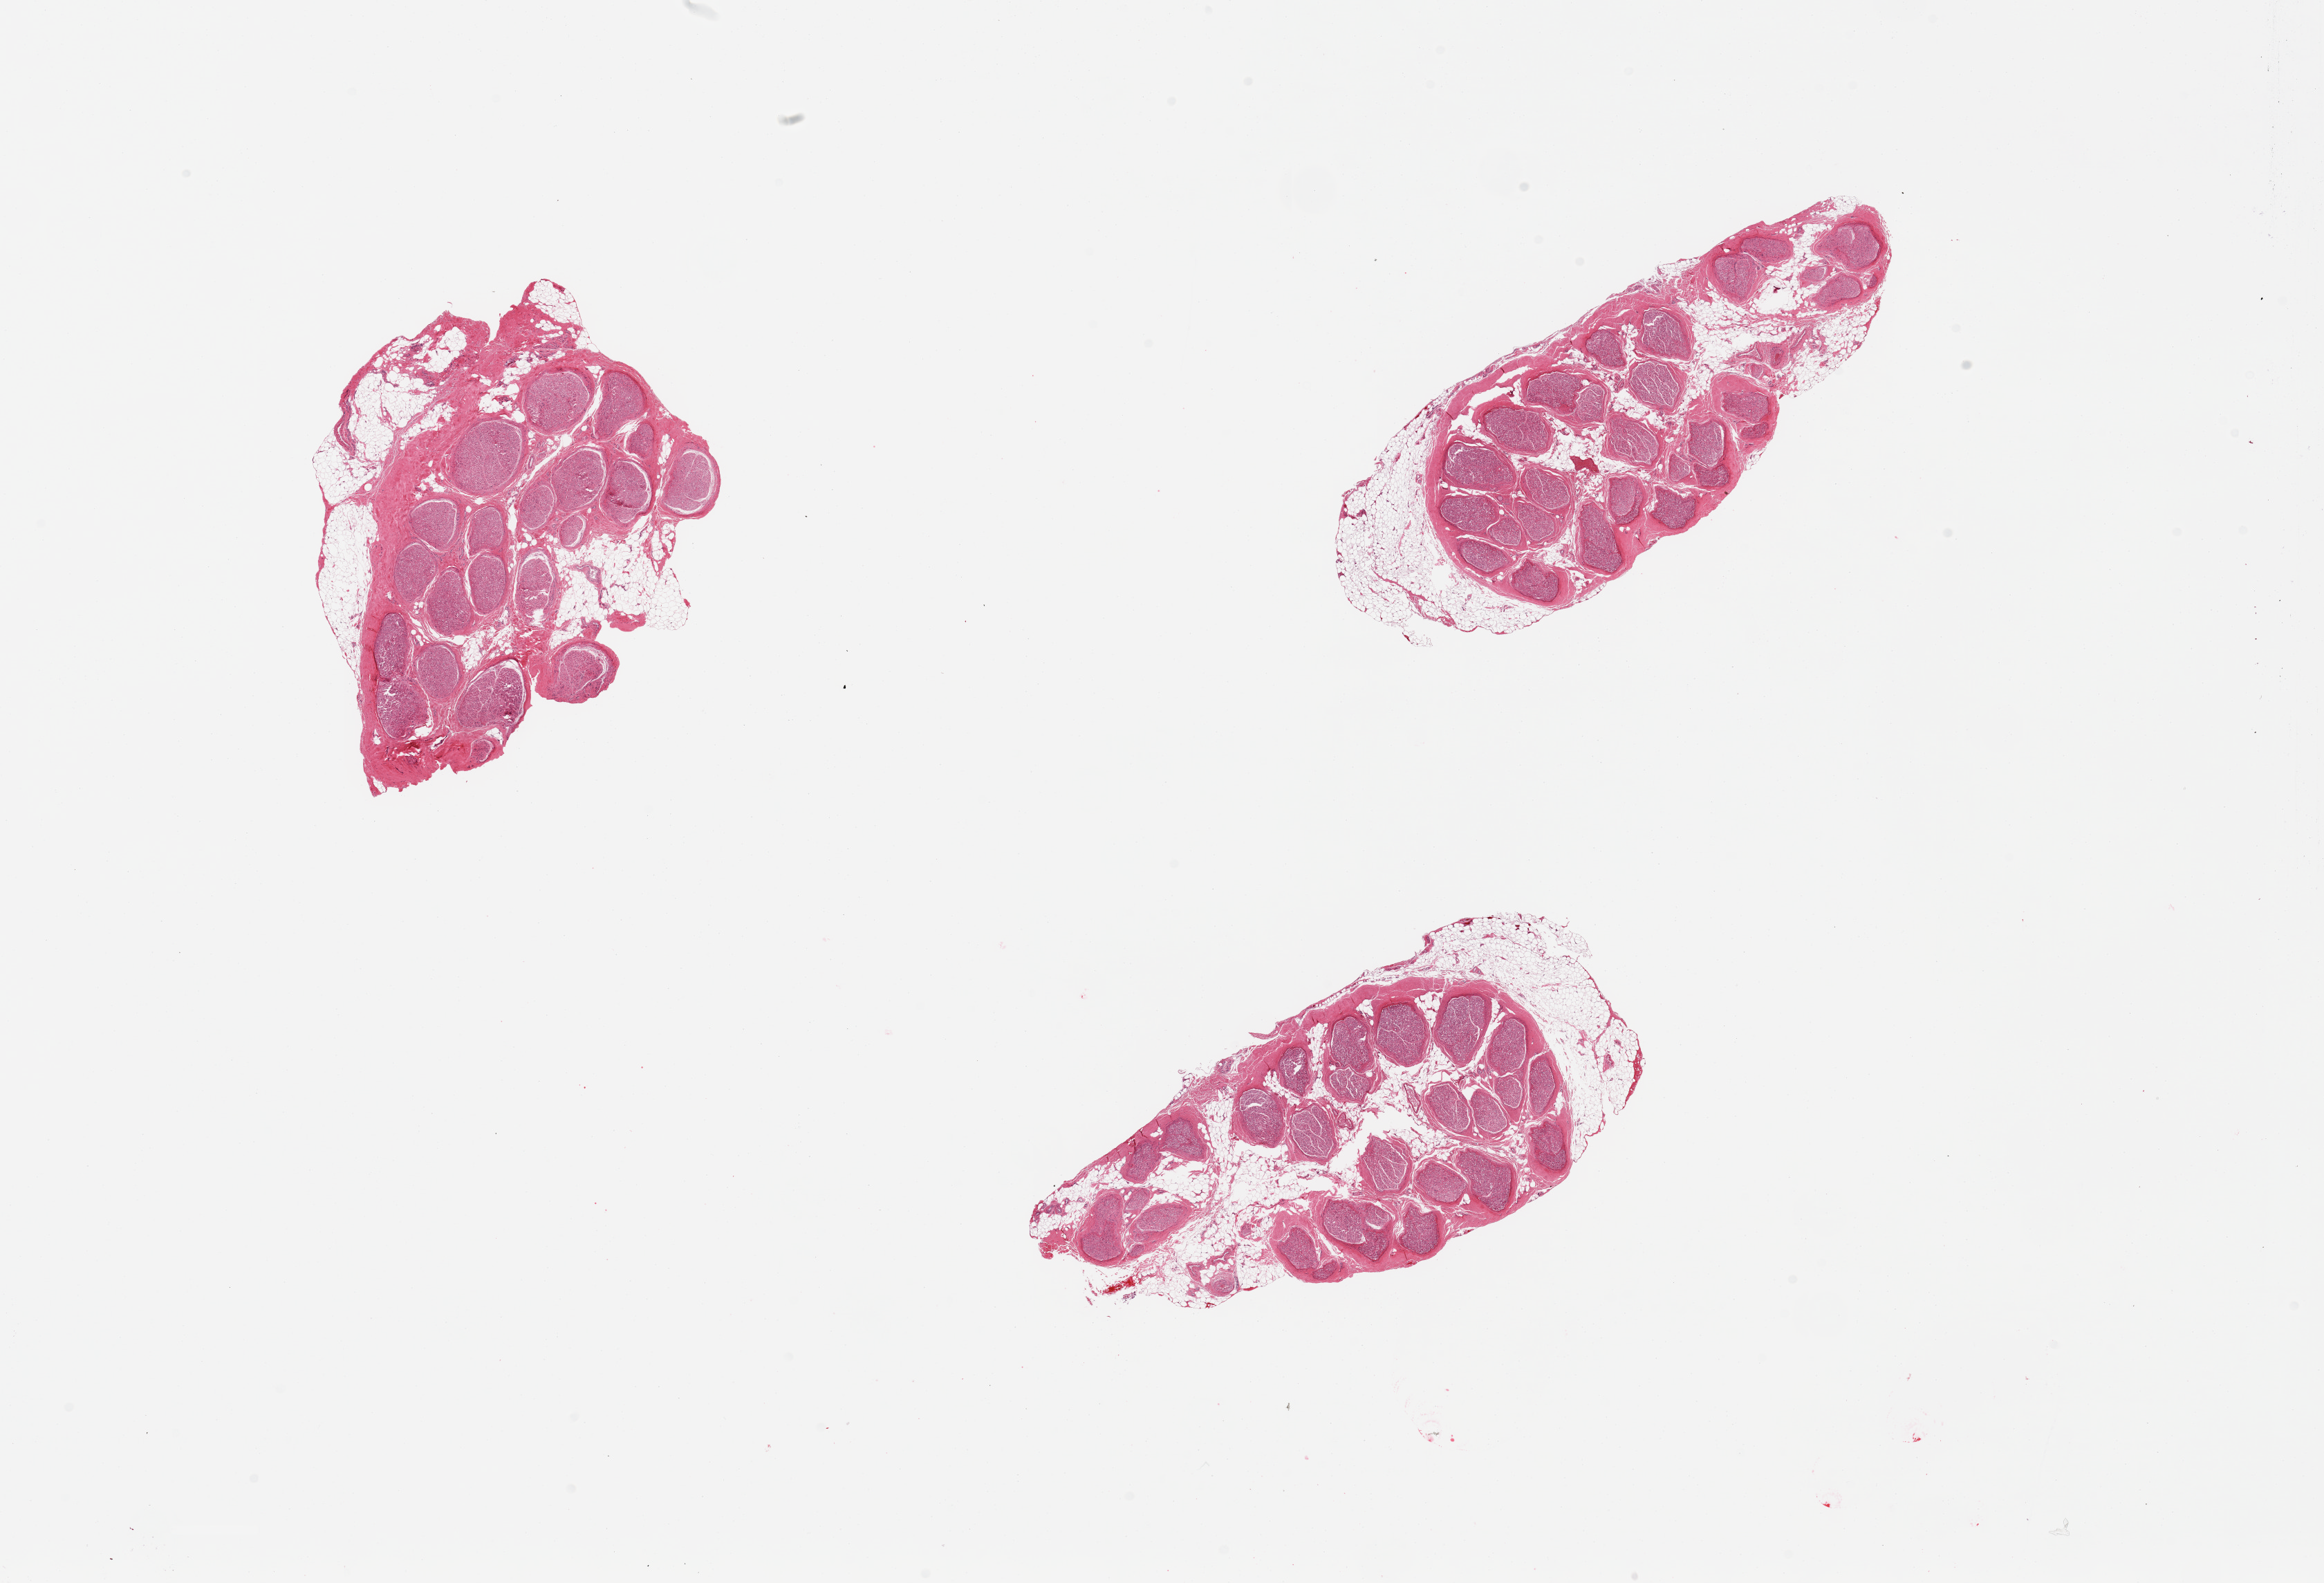
Digitized H&E-stained section — low-resolution overview of the scanned area, about 26.6 x 18.1 mm (from a 20x scan), PAXgene-fixed paraffin-embedded (PFPE) section, section of tibial nerve (target tissue), donor tissue sample. Male donor.
Reviewer comment on this tissue sample: 3 pieces; up to 20% internal fat; up to 1 mm external fat.